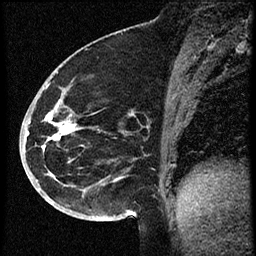
Breast MRI (dynamic contrast-enhanced), one sagittal slice. Position 29 of 60 along the scan axis. Dynamic contrast-enhanced study with each time point stored as its own series, time point 2 of 3 at this slice position (early post-contrast, ordered by acquisition time). 1.5 T. TE 4.2 ms, TR 18.9 ms. 2 mm slice thickness. 256 × 256 image matrix. Female patient. Case-level facts recorded for this patient, not image findings: setting: breast cancer imaged before/during neoadjuvant chemotherapy; receptor status: HR-positive, HER2-negative.
Outlined on this slice (semi-automatically segmented with operator editing):
- analysis volume of interest (the breast-tissue region the enhancement analysis was run in; not a lesion): bounding box [x1, y1, x2, y2] px = [30, 87, 105, 173]
- tumour enhancement mask (voxels above the 100 % enhancement threshold inside the analysis volume of interest): [49, 112, 75, 140]